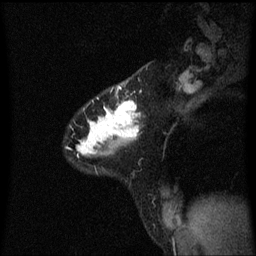
Breast MRI (dynamic contrast-enhanced), one sagittal slice; slice 45 of 60 in the series (ordered by position); dynamic contrast-enhanced series, image 2 of 3 at this slice position (ordered by acquisition); 1.5 T; TE 4.2 ms, TR 8.4 ms; 2 mm slice thickness; 256 × 256 image matrix, field of view 200 × 200 mm. Patient: female, 32 years.
Outlined on this slice (semi-automatically segmented with operator editing):
- analysis volume of interest (the breast-tissue region the enhancement analysis was run in; not a lesion): box from (x=78, y=78) to (x=140, y=157) px
- tumour enhancement mask (voxels above the 70 % enhancement threshold inside the analysis volume of interest): (x=78, y=88)–(x=140, y=157)